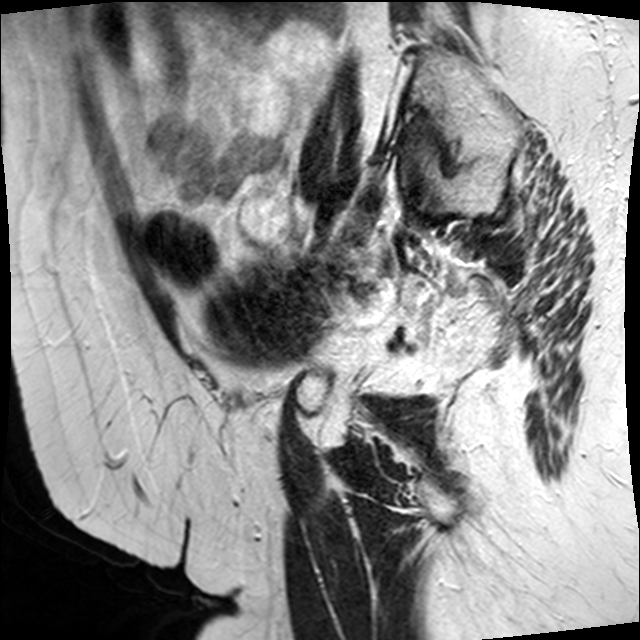
Pelvic MRI for cervical cancer, one sagittal slice; T2-weighted; 1.5 T; TE 89 ms, TR 4610 ms; 4 mm slice thickness; 640 × 640 image matrix. Female patient, age 50 years.
Annotated regions visible in this slice (expert manual segmentation):
- uterus and cervix: box from (x=209, y=261) to (x=334, y=366) px